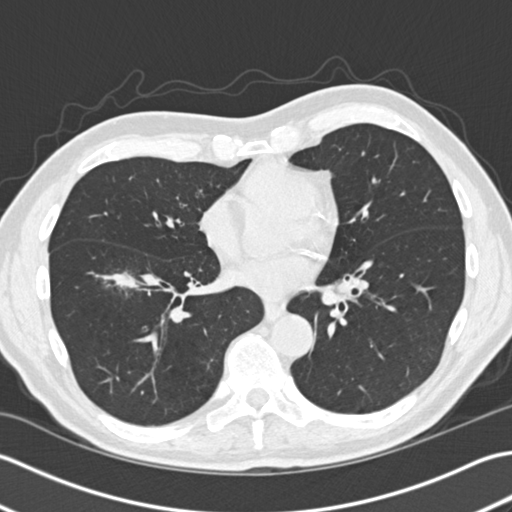
Chest CT (low-dose screening protocol), one axial image. Second annual screen. Lung window (W 1500 / L -600 HU). 2 mm slice thickness. Standard (soft-tissue) reconstruction kernel (B30f). Slice 100 of 172 in the series. Male participant, aged 73 years at enrolment.
• Lesion marked by an expert reader, bounding box <91,253,150,314> (left, top, right, bottom; pixels).
• Screening reader's record for this exam (one nodule recorded; not confirmed to be the boxed lesion): non-calcified nodule or mass ≥4 mm, right lower lobe, 18 × 15 mm, spiculated (stellate) margins, soft tissue attenuation, pre-existing on the prior screen: yes.
• Official screen result: positive, other.
• Participant outcome: lung cancer diagnosed 87 days after this screen — non-small cell carcinoma, right lower lobe, stage IA (AJCC 6th edition), 30 mm at pathology.